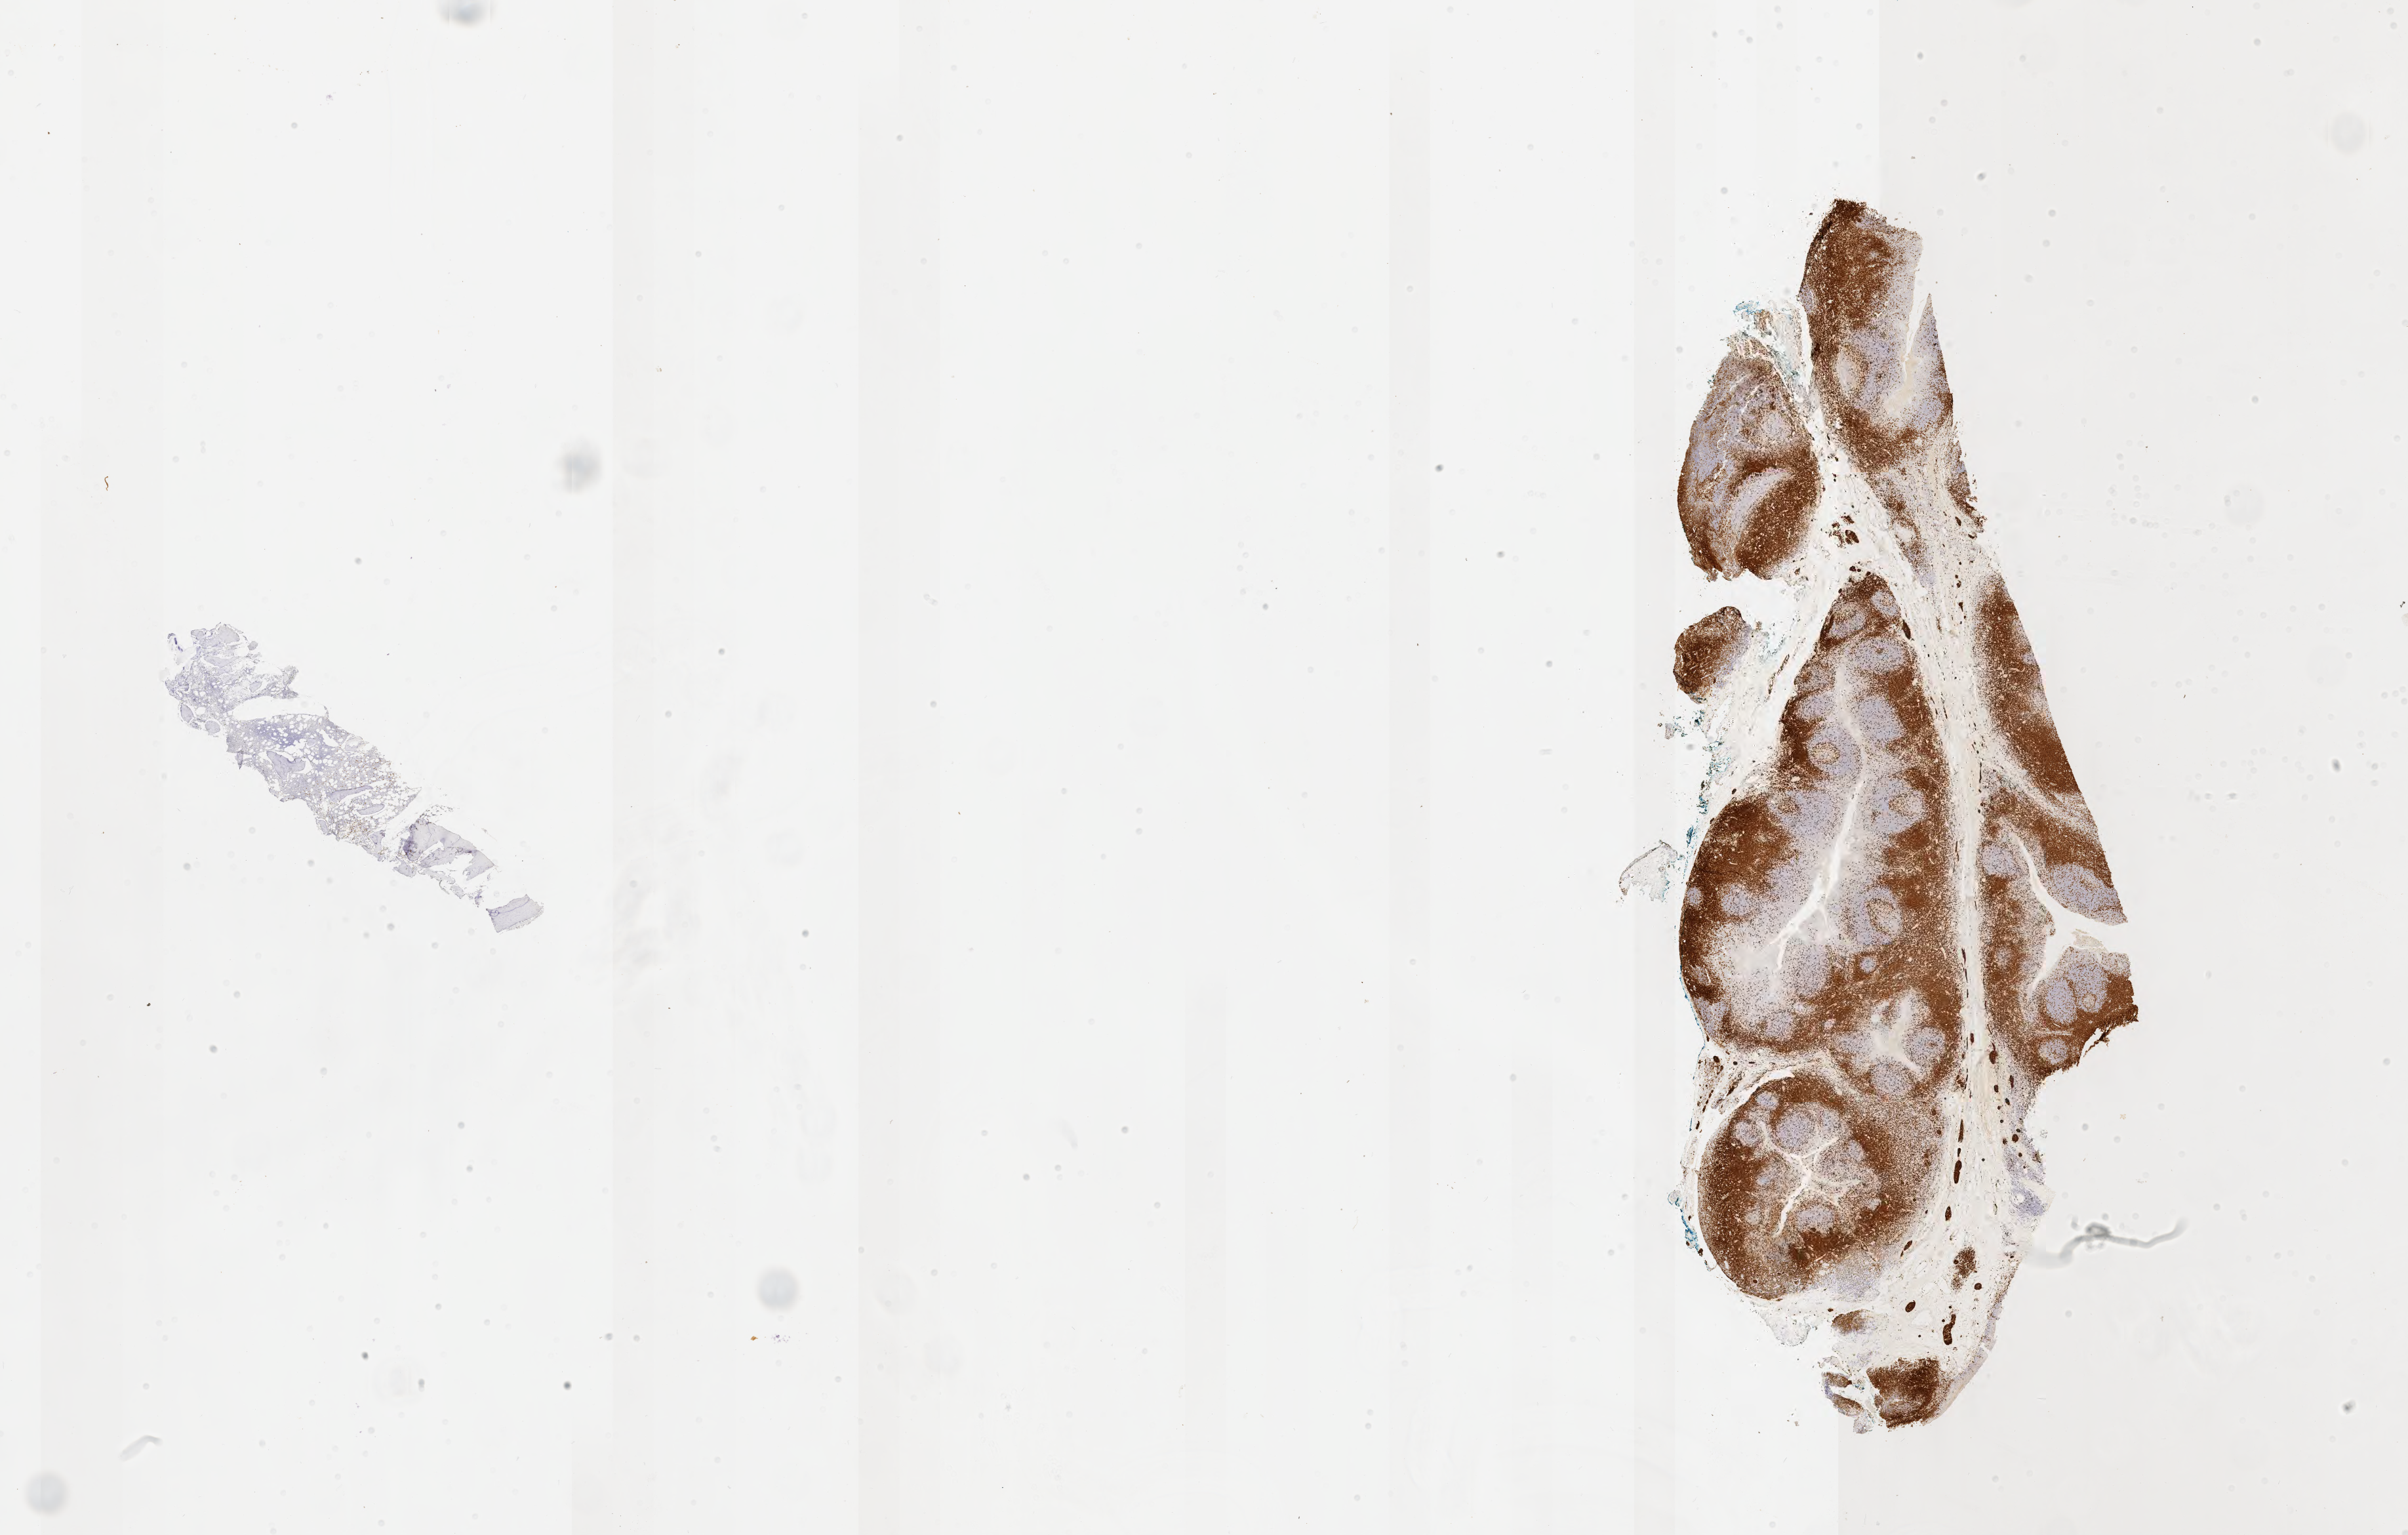
Immunohistochemistry (IHC) whole-slide image stained for CD3 — whole scanned area (about 29.7 x 18.9 mm) shown as a low-resolution overview; specimen: tumor tissue; site: bone marrow. Patient: female, age at initial diagnosis 4 years.
Diagnosis: Burkitt lymphoma, NOS.